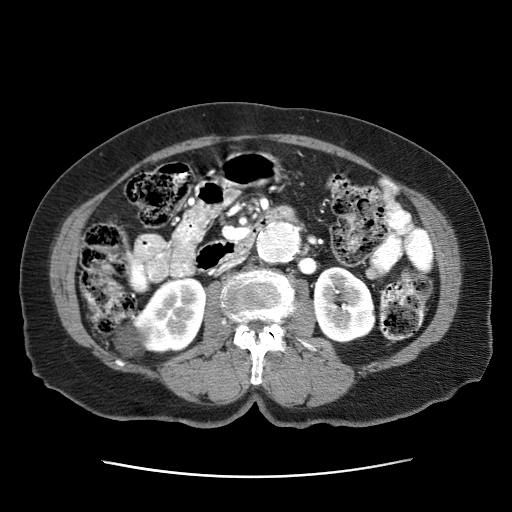
Contrast-enhanced abdominal CT (liver protocol), one axial slice. Intravenous contrast given. Soft-tissue window (W 400 / L 40 HU). 512 × 512 image matrix, field of view 360 × 360 mm. Patient: female, 79 years. From the clinical record (not read from this slice): diagnosis: hepatocellular carcinoma (patient treated with transarterial chemoembolisation; whether this scan precedes or follows treatment is not stated here); TNM stage (as recorded): Stage-II; Child-Pugh class: B; tumour differentiation: well differentiated; tumour nodularity: multinodular.
Annotated regions visible in this slice (semi-automatically segmented with operator editing):
- abdominal aorta: bounding box (x1, y1, x2, y2) in pixels: (257, 224, 300, 263)